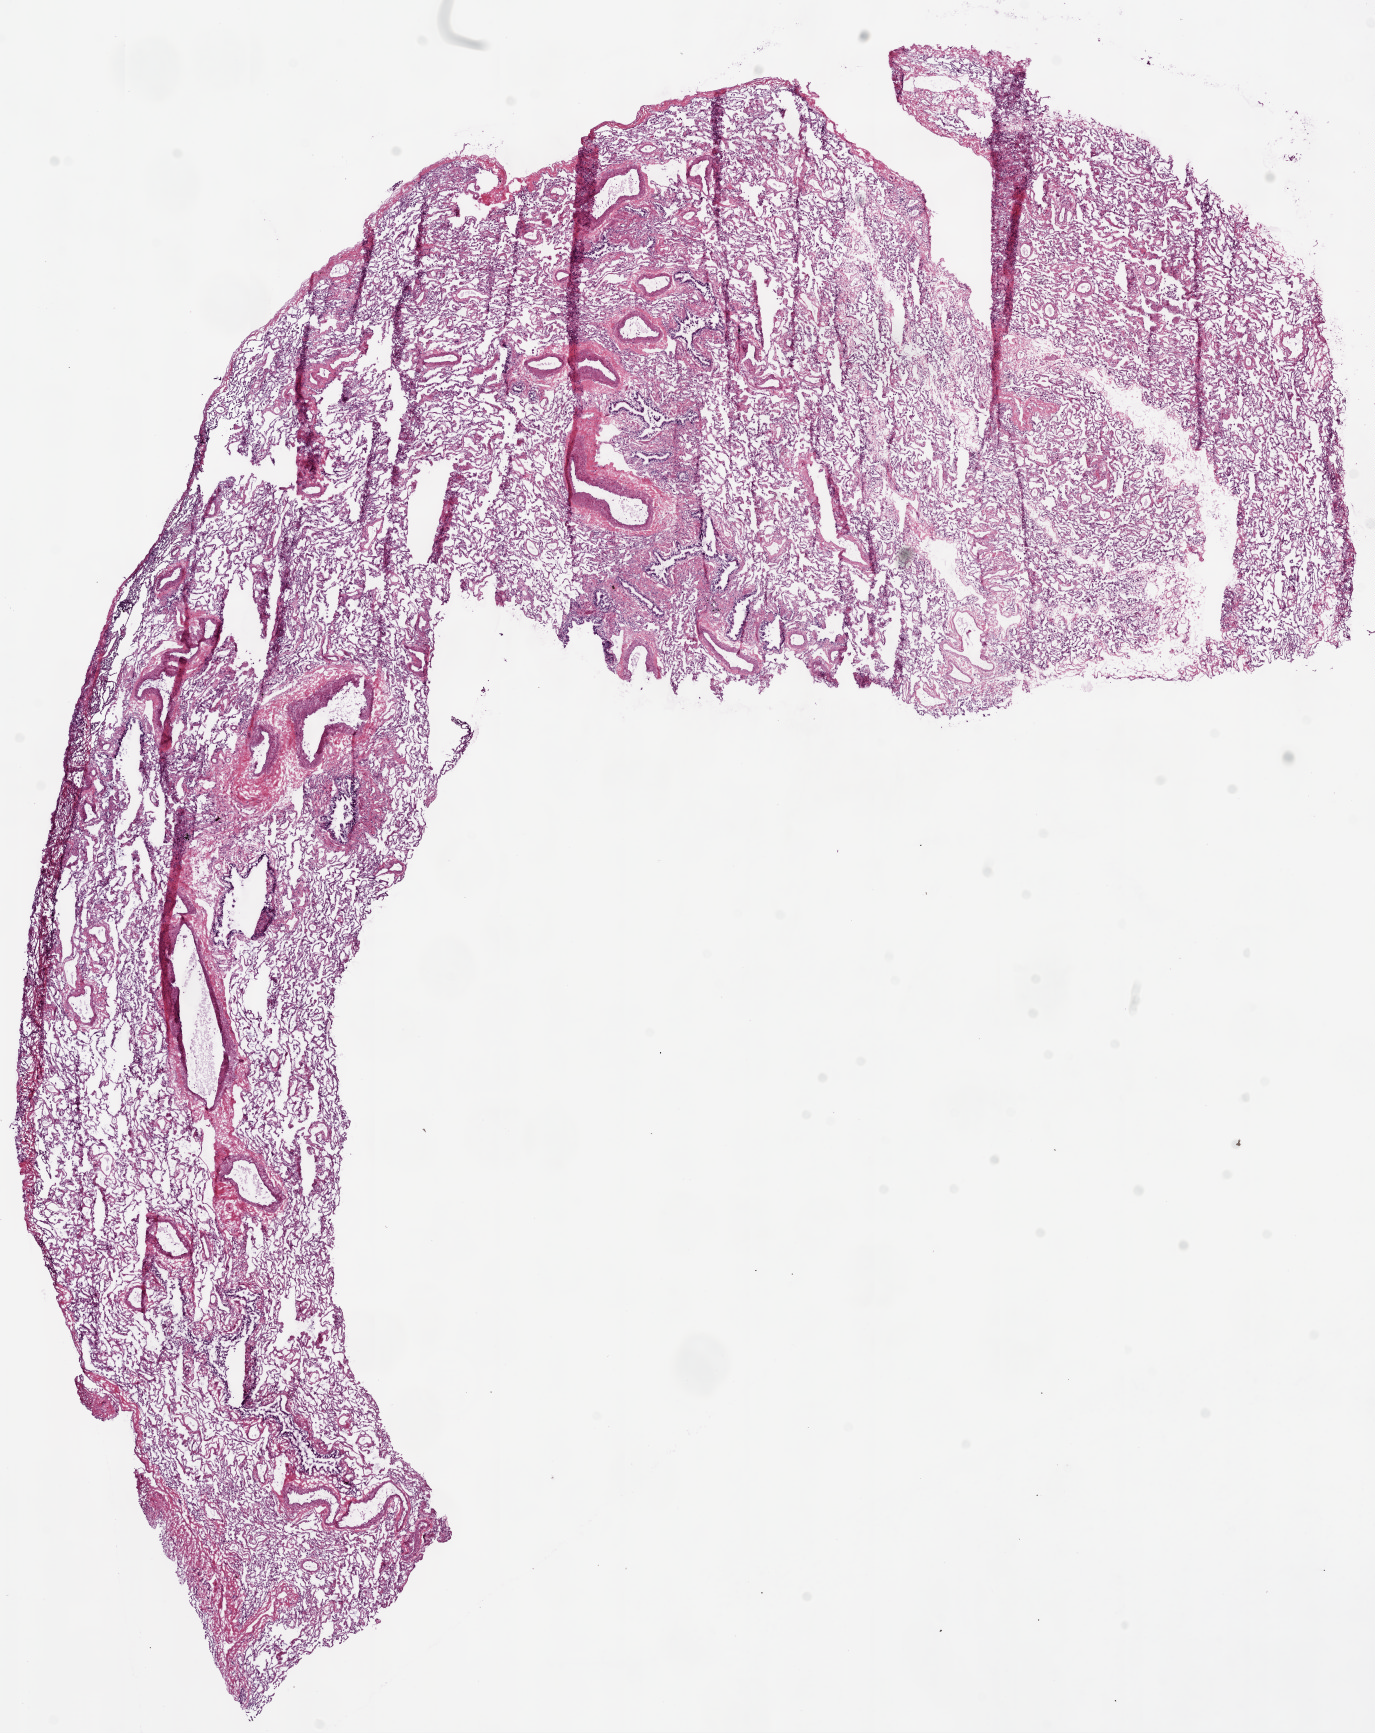
Whole-slide histology image, H&E — shown as a low-resolution overview of the whole scanned area (about 11.0 x 13.9 mm, from a 20x scan). Frozen section from the bottom of the tissue portion. Solid tissue normal (non-tumour tissue) sample from the lung. Male patient; age at initial diagnosis 68 years.
This section: solid tissue normal (non-tumour) sample from the same patient. Patient diagnosis: Squamous cell carcinoma, NOS (upper lobe, lung).